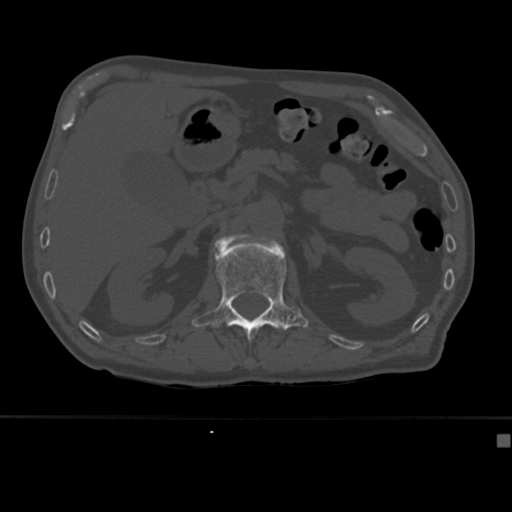
CT including the spine, one axial slice. Position 170 of 430 along the scan axis. Reconstruction kernel Br40s. Bone window (W 1800 / L 400 HU). 1.5 mm slice thickness. 512 × 512 image matrix. Patient: male, 64 years. Case-level facts recorded for this patient, not image findings: primary cancer: uterus.
Annotated regions visible in this slice (semi-automatically segmented with operator editing):
- L1 vertebra: bounding box [x1, y1, x2, y2] px = [192, 233, 308, 341]